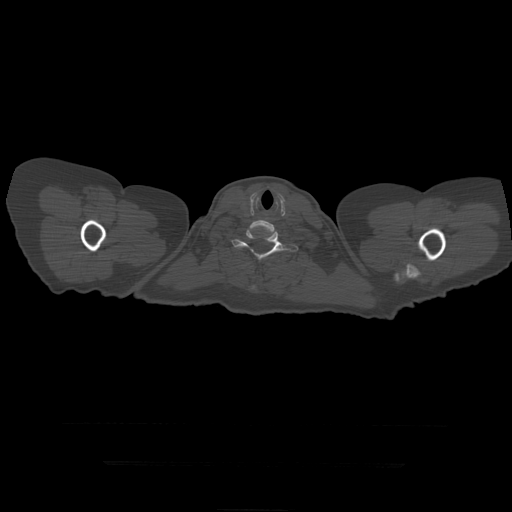
CT including the spine, one axial slice. Slice 392 of 399 in the series (ordered by position). 120 kVp. Bone window (W 1800 / L 400 HU). 512 × 512 image matrix. Patient age 41 years. From the clinical record (not read from this slice): primary cancer: breast.
Outlined on this slice (semi-automatic segmentation, software-assisted and operator-edited):
- T1 vertebra: bounding box [x1, y1, x2, y2] px = [232, 230, 299, 260]